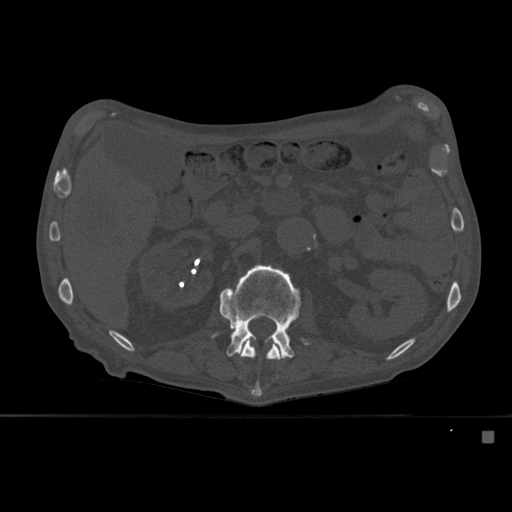
CT including the spine, one axial slice; slice 242 of 527 in the series (ordered by position); bone window (W 1800 / L 400 HU); 512 × 512 image matrix, field of view 373 × 373 mm. Male patient, age 78 years. From the clinical record (not read from this slice): primary cancer: prostate.
Structures marked on this image (semi-automatic segmentation, software-assisted and operator-edited):
- L1 vertebra: bounding box [x1, y1, x2, y2] px = [241, 340, 282, 397]
- L2 vertebra: [212, 264, 312, 359]